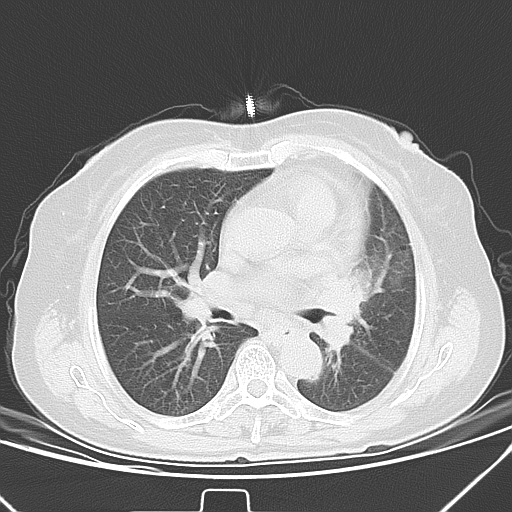
Chest CT, one axial slice. Position 22 of 40 along the scan axis. 120 kVp. Lung window (W 1500 / L -600 HU). 5 mm slice thickness. 512 × 512 image matrix, field of view 331 × 331 mm. Female patient, age 59 years. Case-level facts recorded for this patient, not image findings: clinical TNM (as recorded): T3 N1 M0; histopathological grade: G3.
Annotated regions visible in this slice (bounding box drawn by a radiologist):
- lung tumour (recorded histology: small cell carcinoma): bounding box [x1, y1, x2, y2] px = [324, 267, 381, 353]